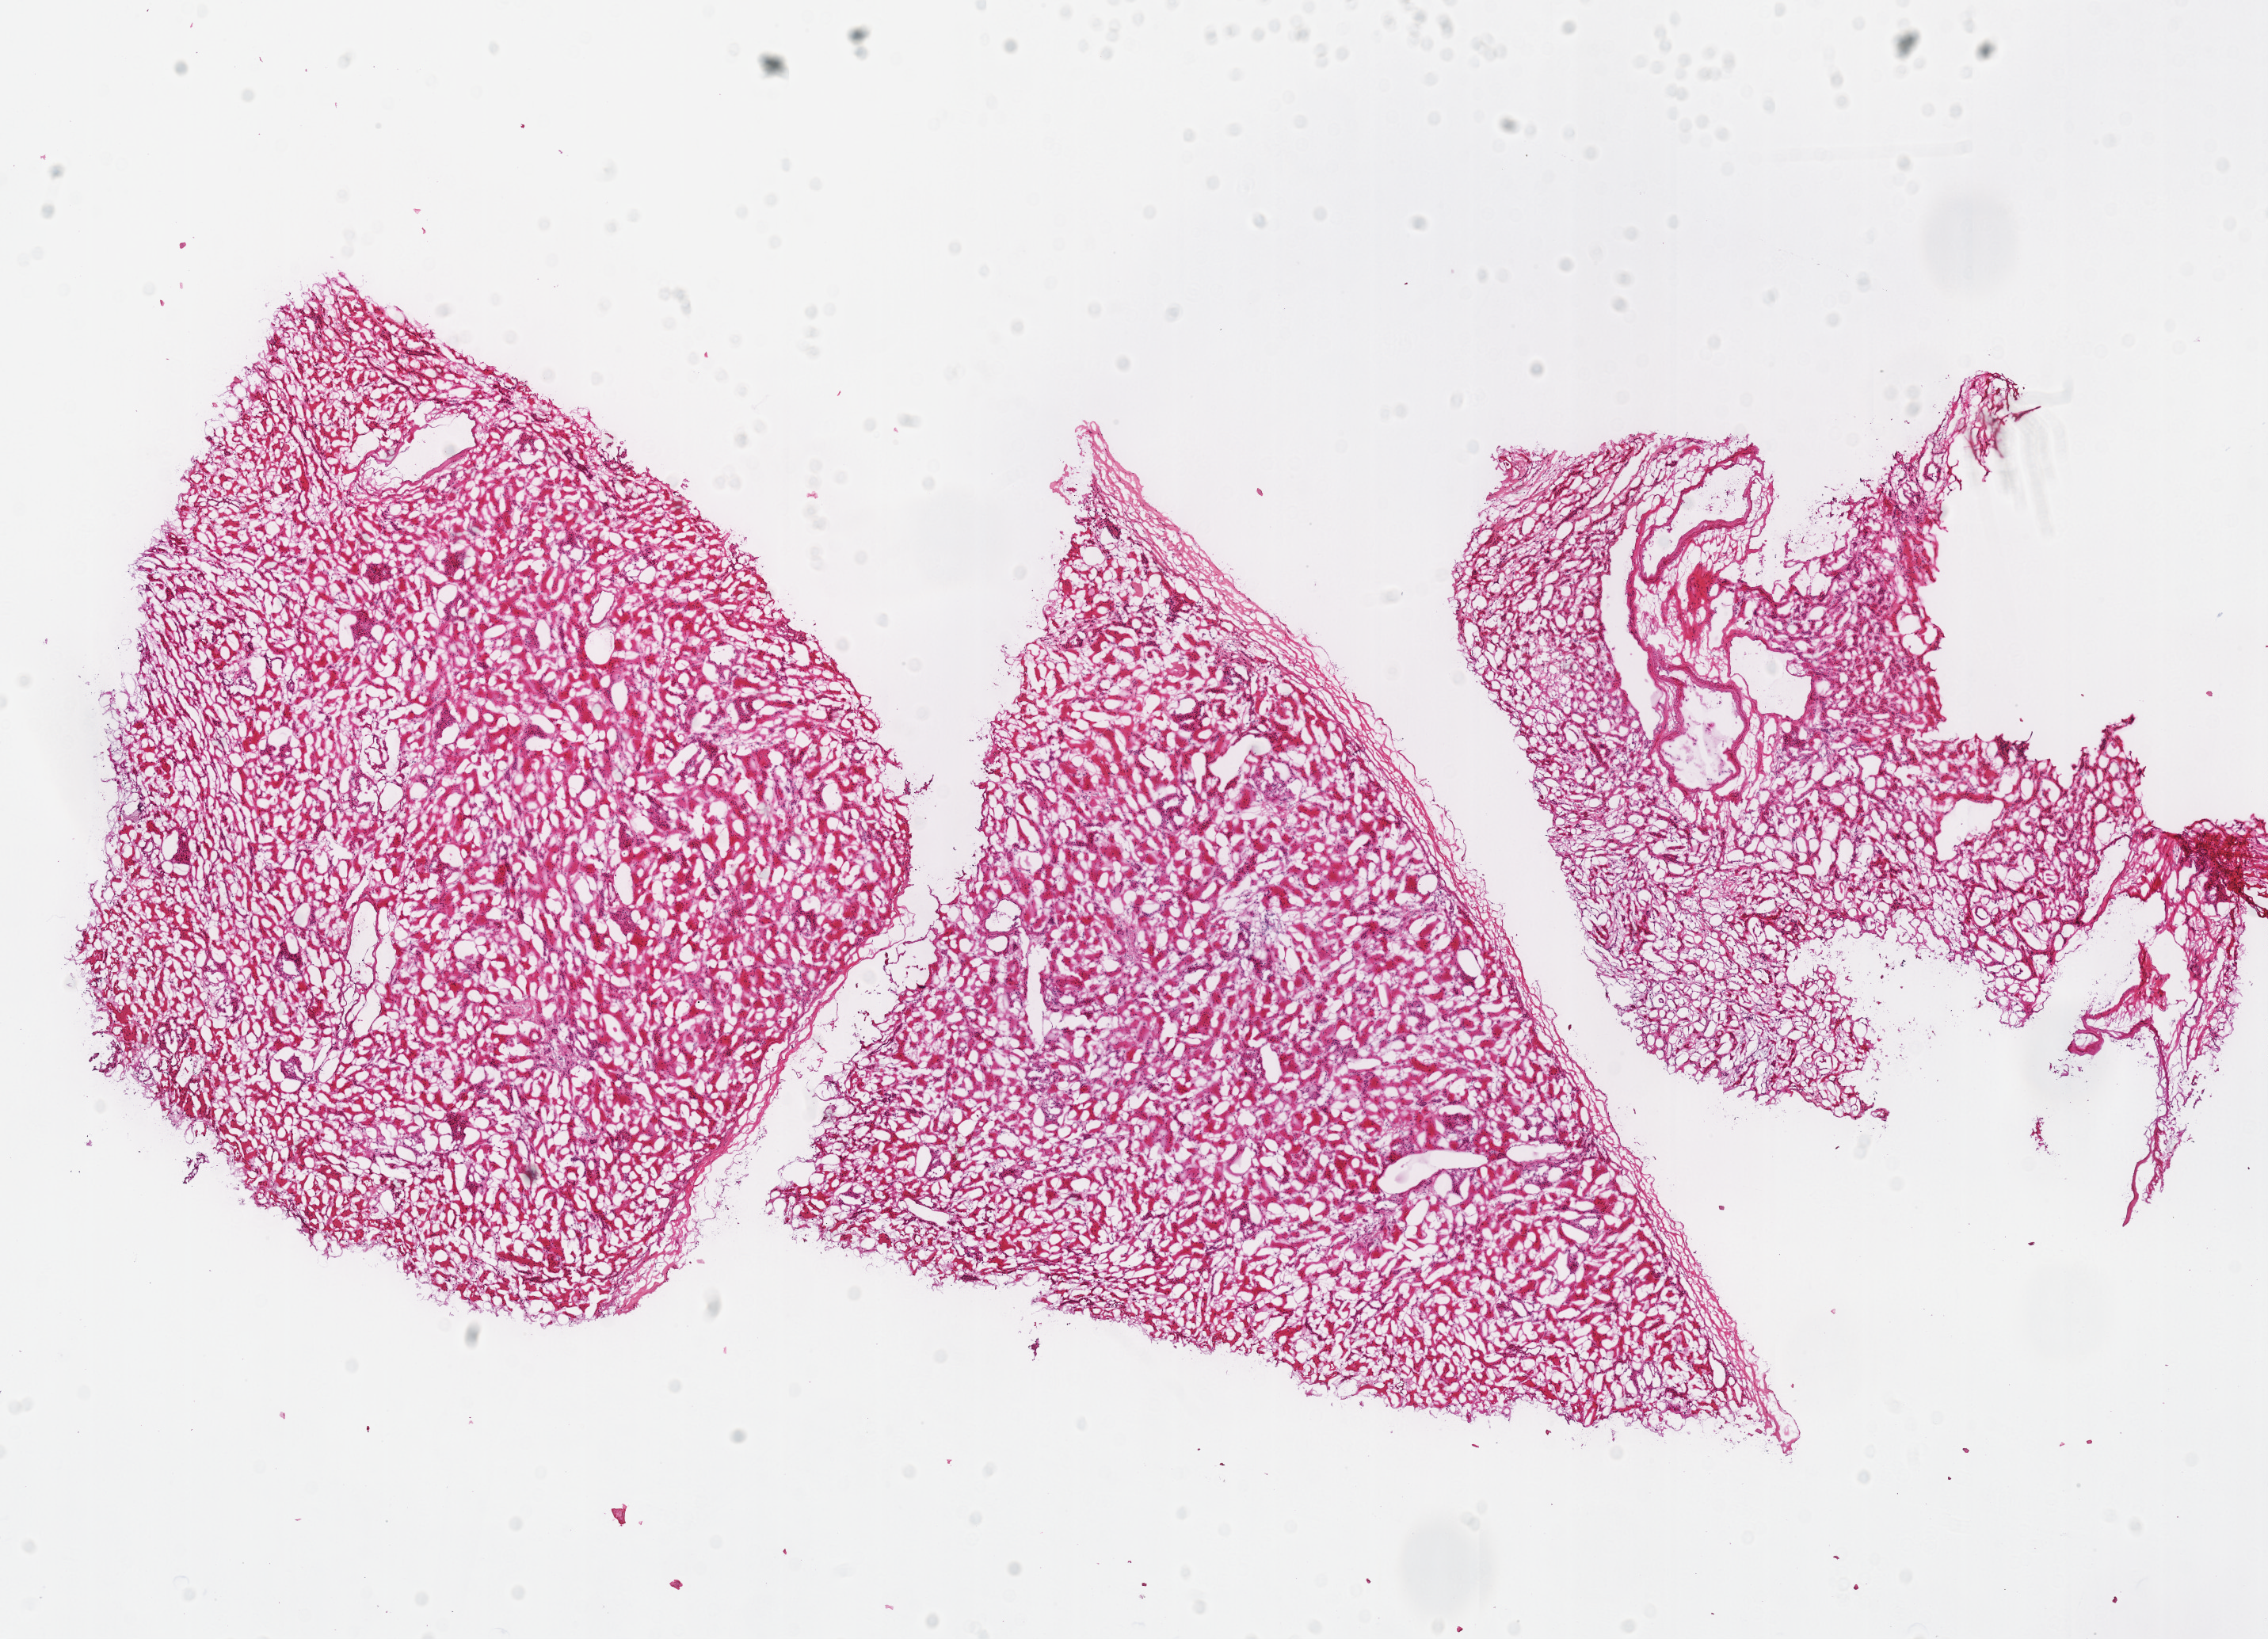
Whole-slide histology image, Hematoxylin and eosin (H&E) stained, a low-resolution overview of the entire scanned area, about 11.3 x 8.1 mm, frozen section, kidney, solid tissue normal (non-tumour tissue) sample. Male, age 49 years at initial diagnosis.
This section: solid tissue normal sample (biorepository sample class). Patient diagnosis: Renal cell carcinoma, chromophobe type.